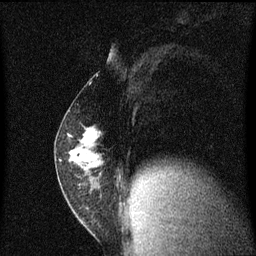
Breast MRI (dynamic contrast-enhanced), one sagittal slice; position 30 of 60 along the scan axis; dynamic contrast-enhanced series, image 2 of 3 at this slice position (ordered by acquisition); 1.5 T; TE 4.2 ms, TR 8.4 ms; 256 × 256 image matrix, field of view 200 × 200 mm. Female patient, age 52 years. Case-level facts recorded for this patient, not image findings: setting: breast cancer imaged before/during neoadjuvant chemotherapy; receptor status: HER2-positive.
Structures marked on this image (semi-automatic segmentation, software-assisted and operator-edited):
- analysis volume of interest (the breast-tissue region the enhancement analysis was run in; not a lesion): box from (x=56, y=124) to (x=107, y=191) px
- tumour enhancement mask (voxels above the 70 % enhancement threshold inside the analysis volume of interest): (x=70, y=128)–(x=97, y=163)